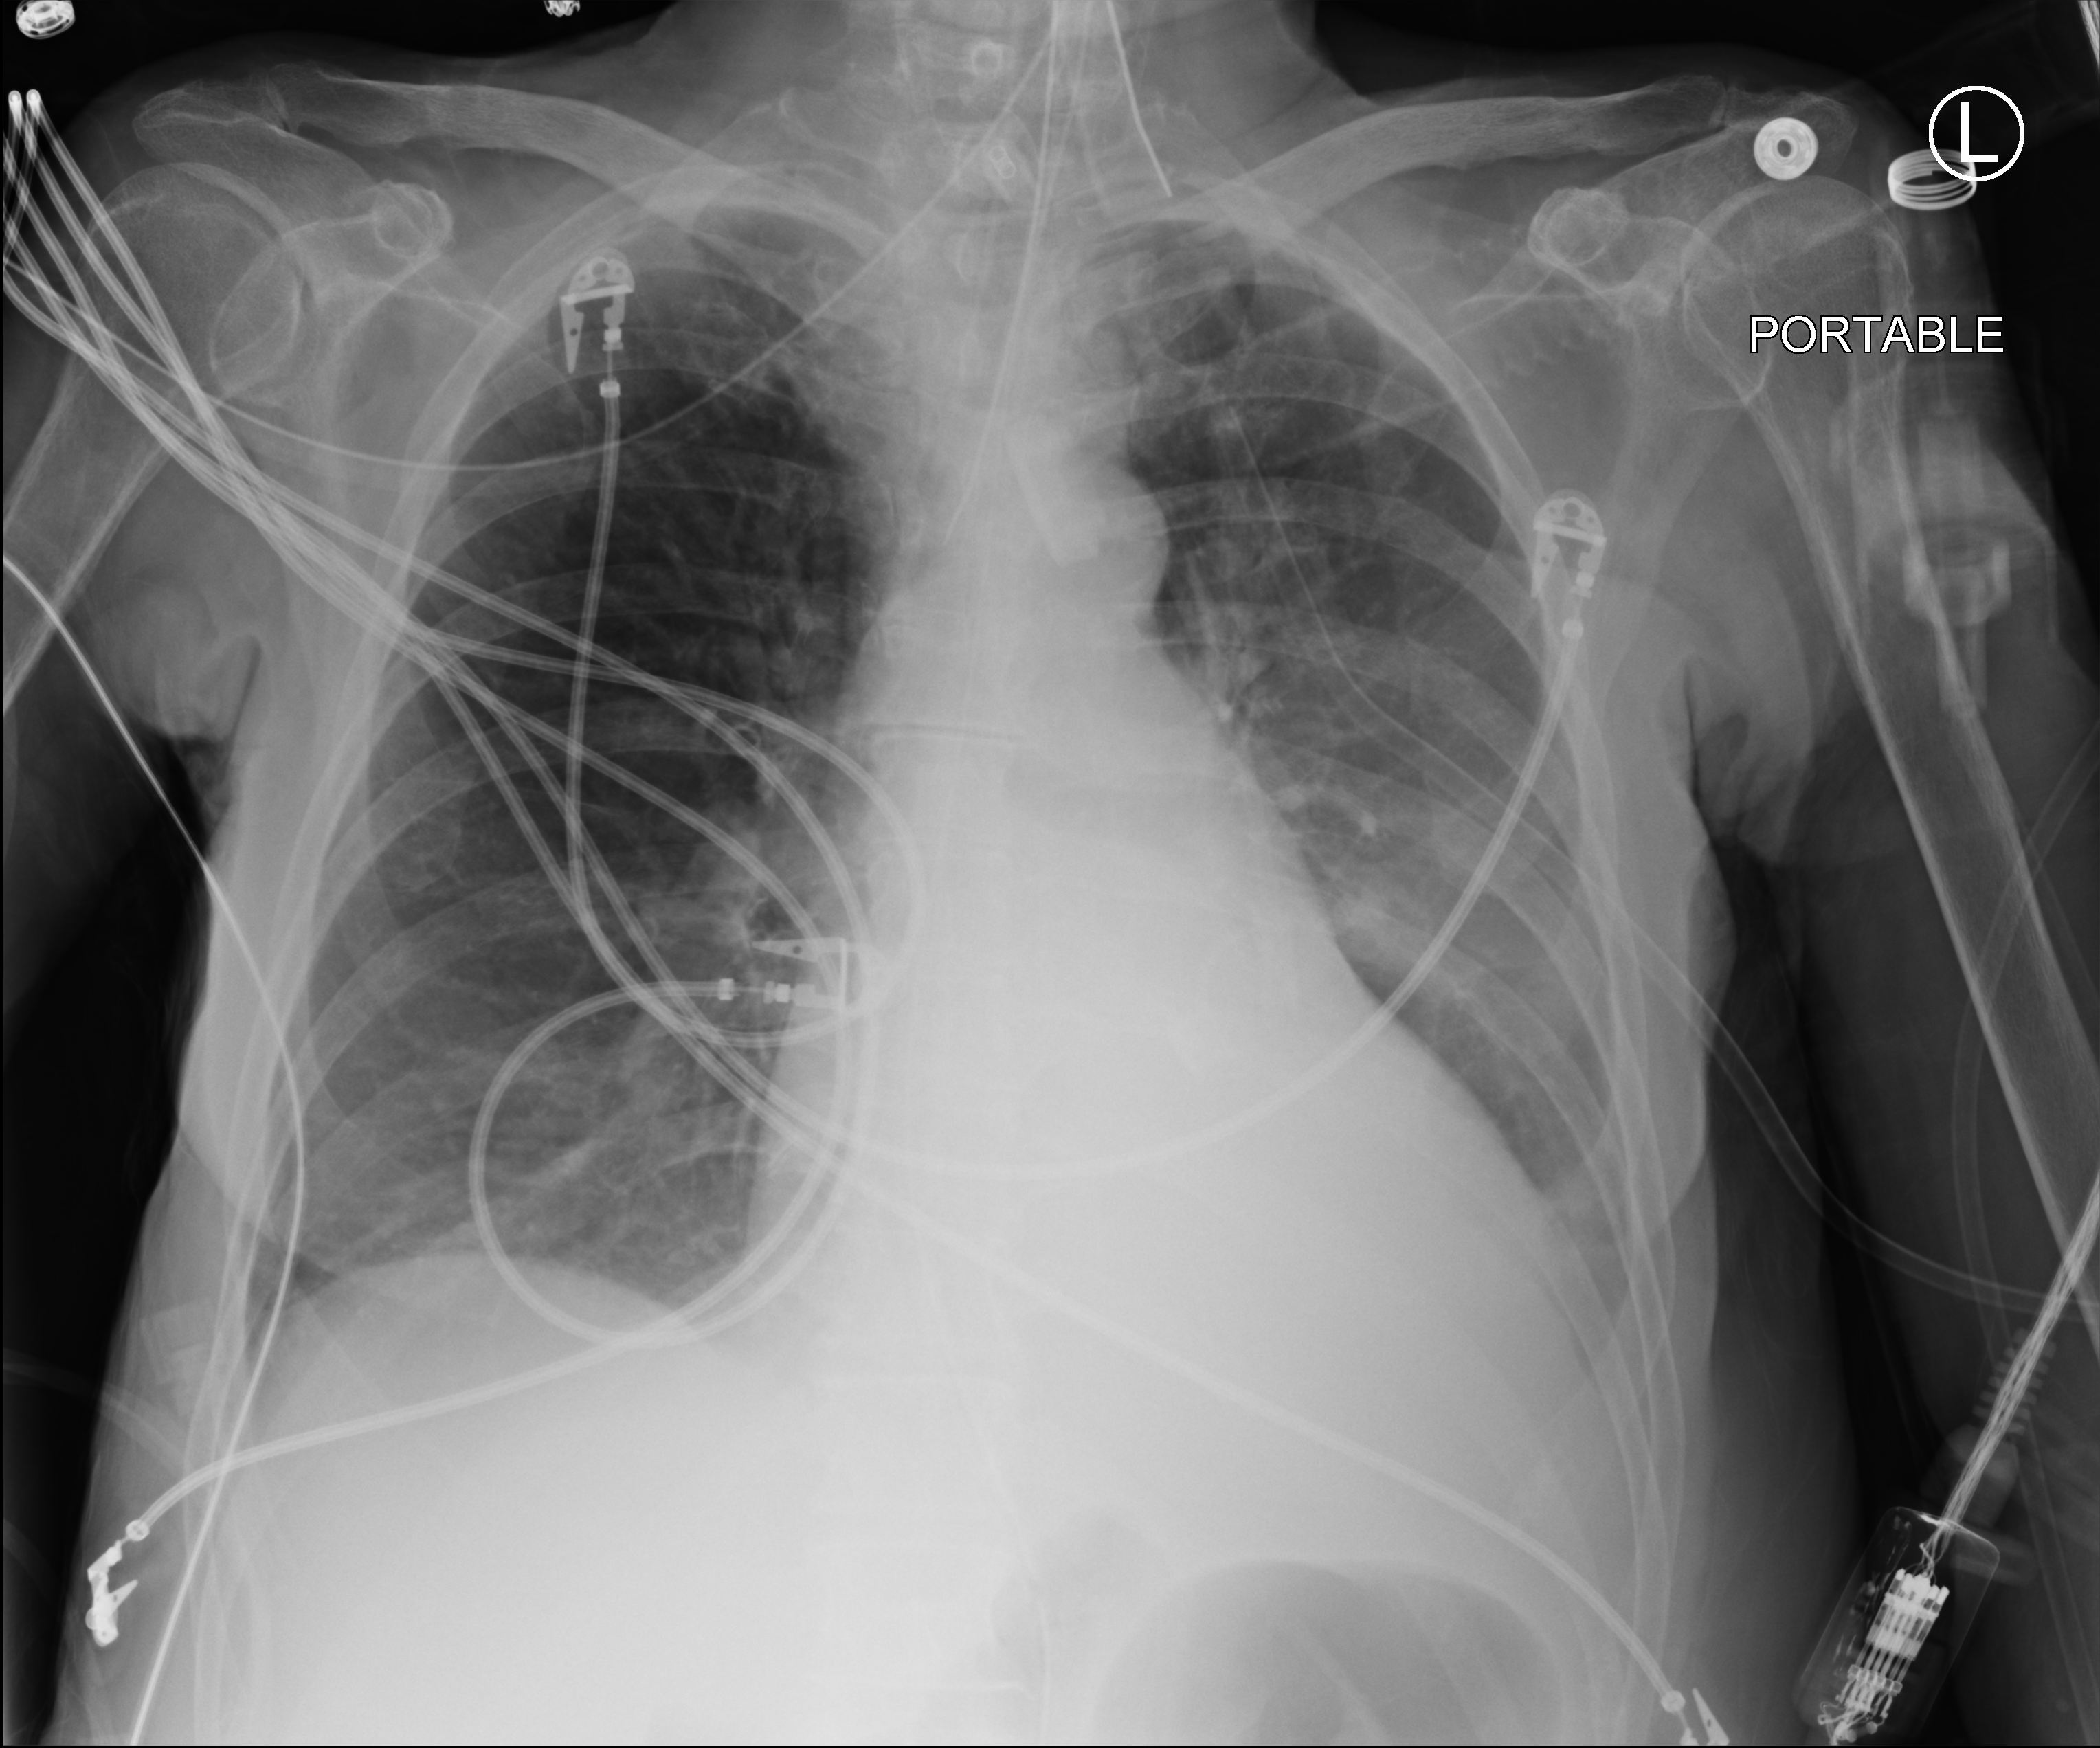
Chest X-ray (portable); anteroposterior (AP) projection. Patient hospitalised with COVID-19; female, aged 60–74 years.
Admission-level facts for this patient (not findings on this image; timing relative to this image not recorded): mechanically ventilated during this hospital stay: yes; admitted to intensive care during this hospital stay: yes.